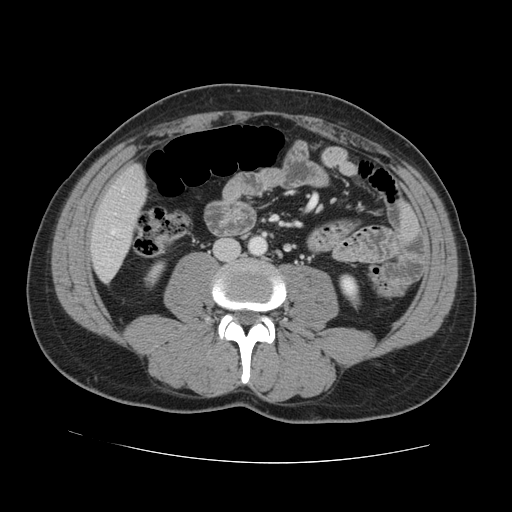
Contrast-enhanced abdominal CT, one axial slice; slice 23 of 131 in the series (ordered by position); 120 kVp; intravenous contrast given; soft-tissue window (W 400 / L 40 HU); 2.5 mm slice thickness; 512 × 512 image matrix. Male patient, age 40 years. From the clinical record (not read from this slice): diagnosis: colorectal cancer liver metastases, imaged before liver resection; multiple liver metastases: yes; largest metastasis: 2.9 cm; chemotherapy before resection: yes.
Annotated regions visible in this slice (manually delineated by an expert):
- hepatic veins: bounding box [x1, y1, x2, y2] px = [111, 230, 114, 234]
- liver: [92, 166, 145, 280]